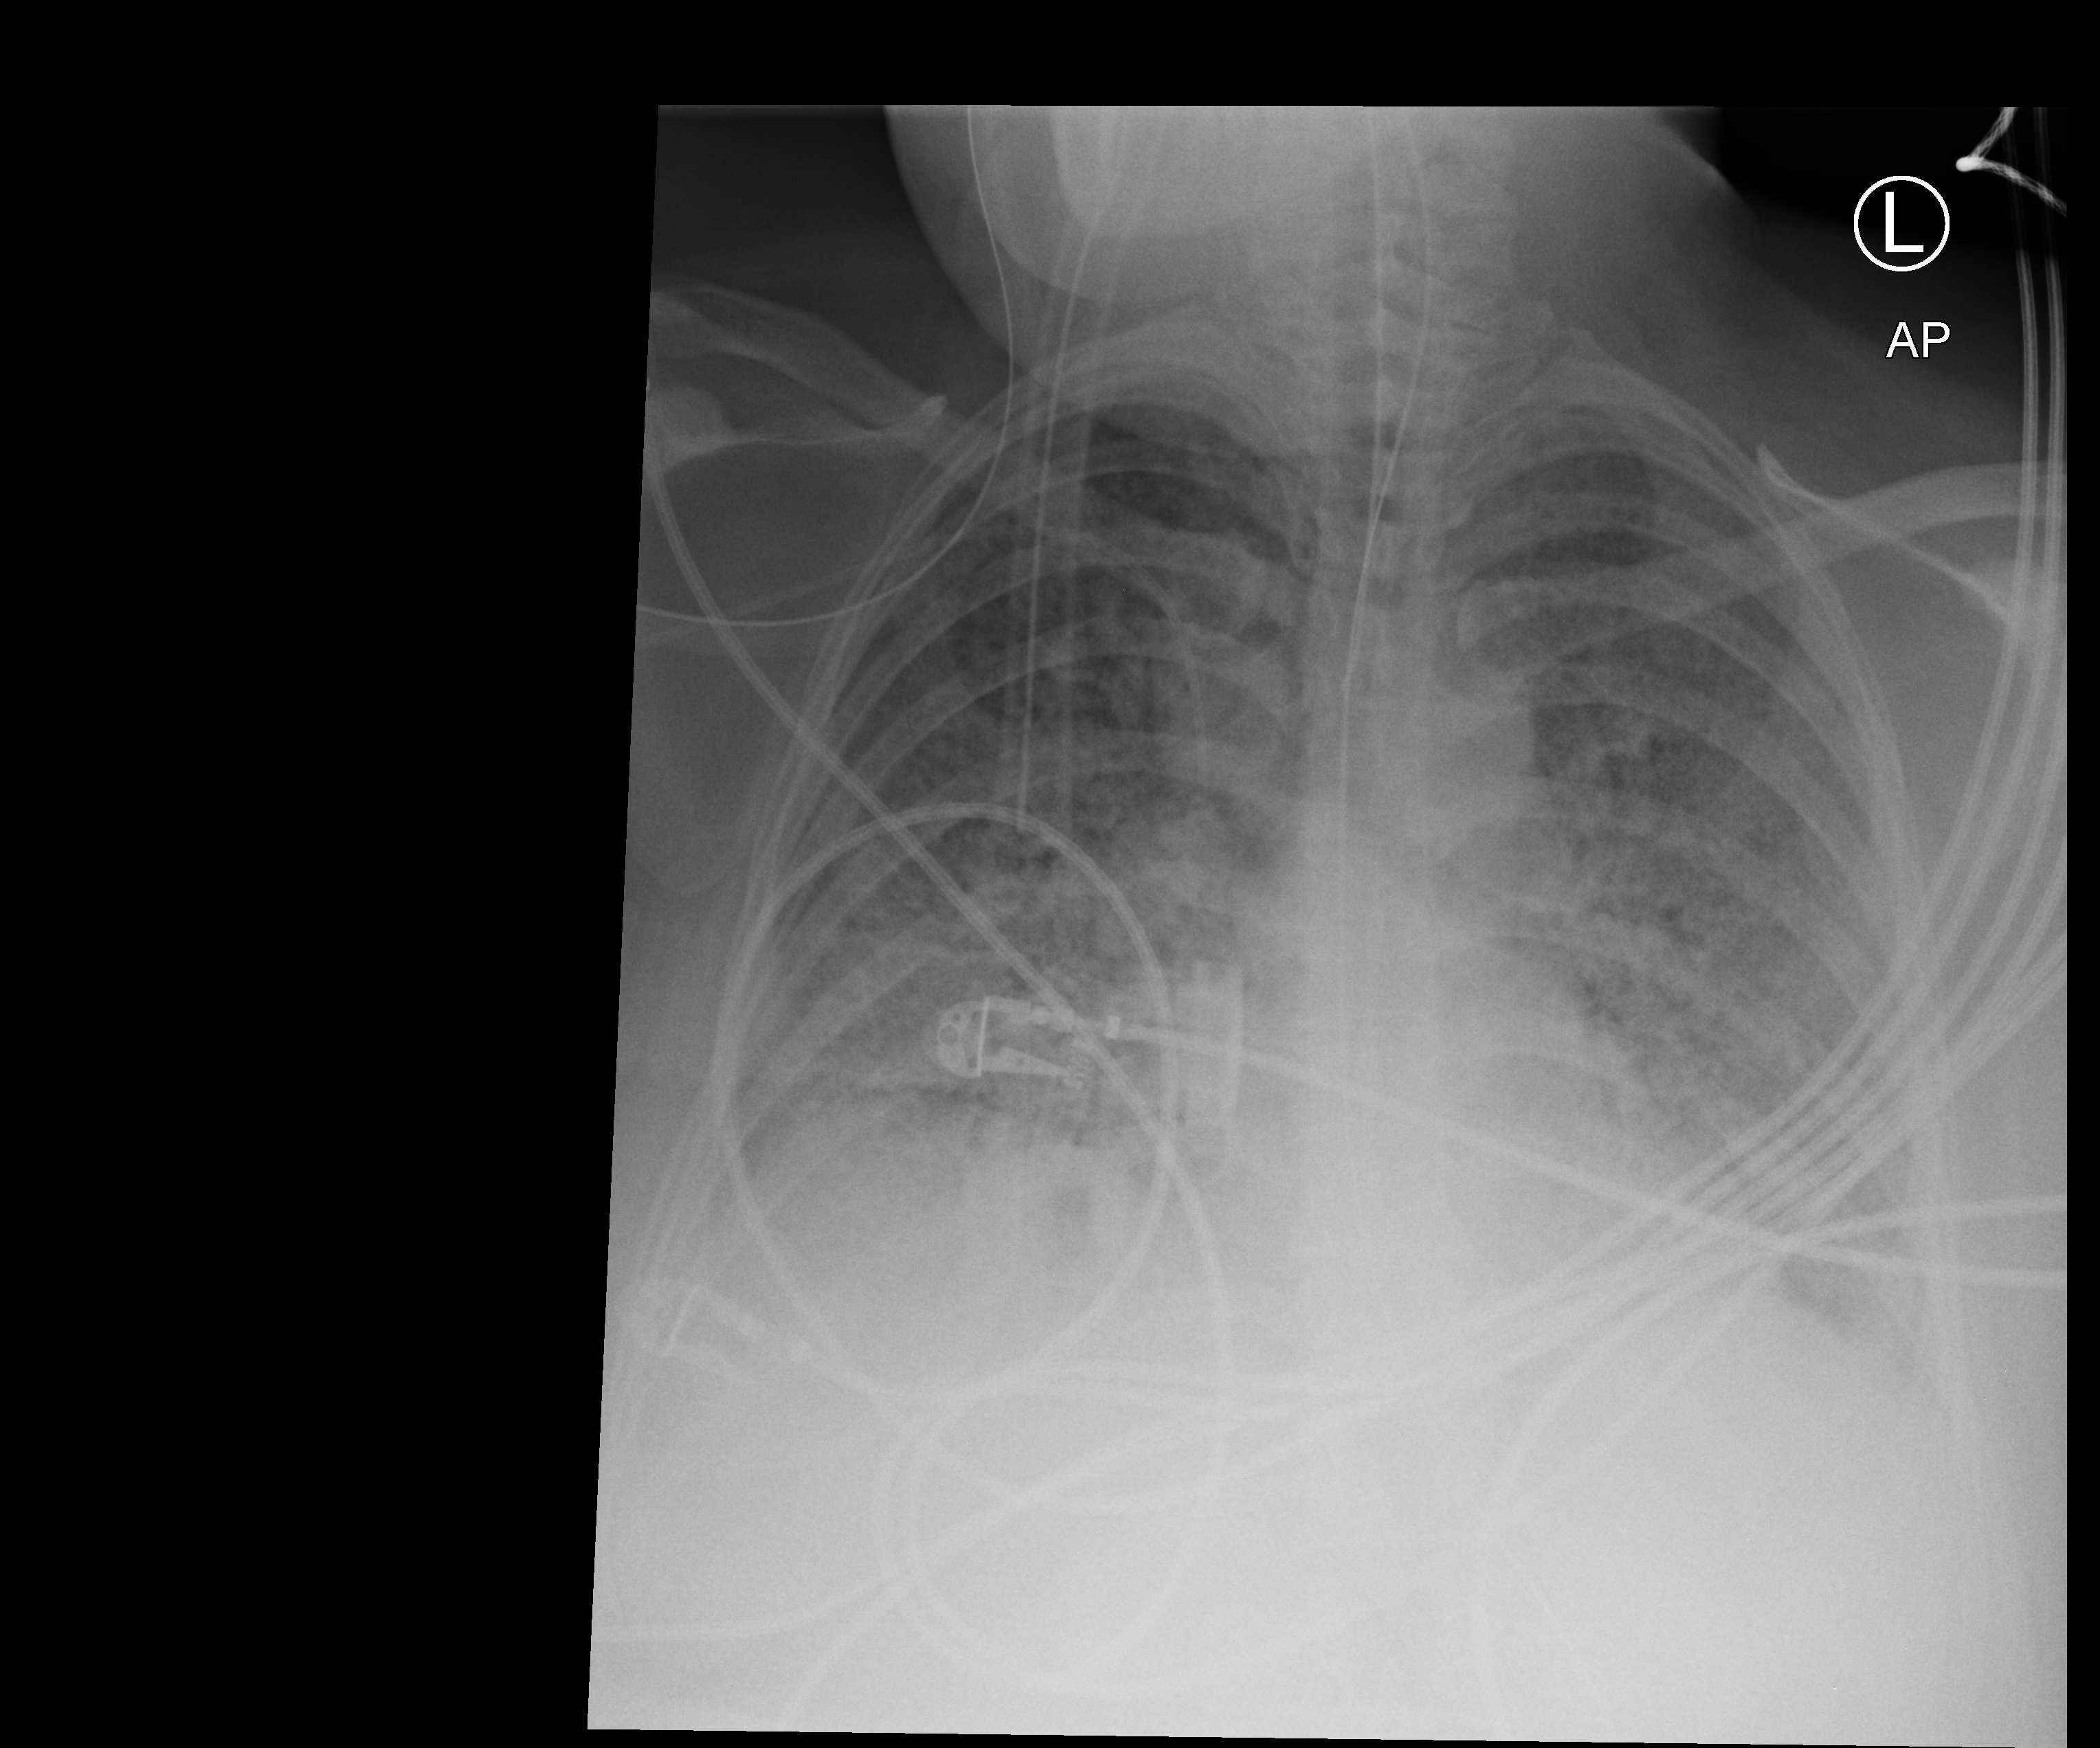
Bedside chest radiograph (computed radiography), anteroposterior (AP) projection. Female patient hospitalised with COVID-19, age 18–59 years.
Hospital-stay facts (about this admission, not read from this image; timing relative to this image not recorded):
- admitted to intensive care during this hospital stay: yes
- diabetes (admission record): no
- mechanically ventilated during this hospital stay: yes